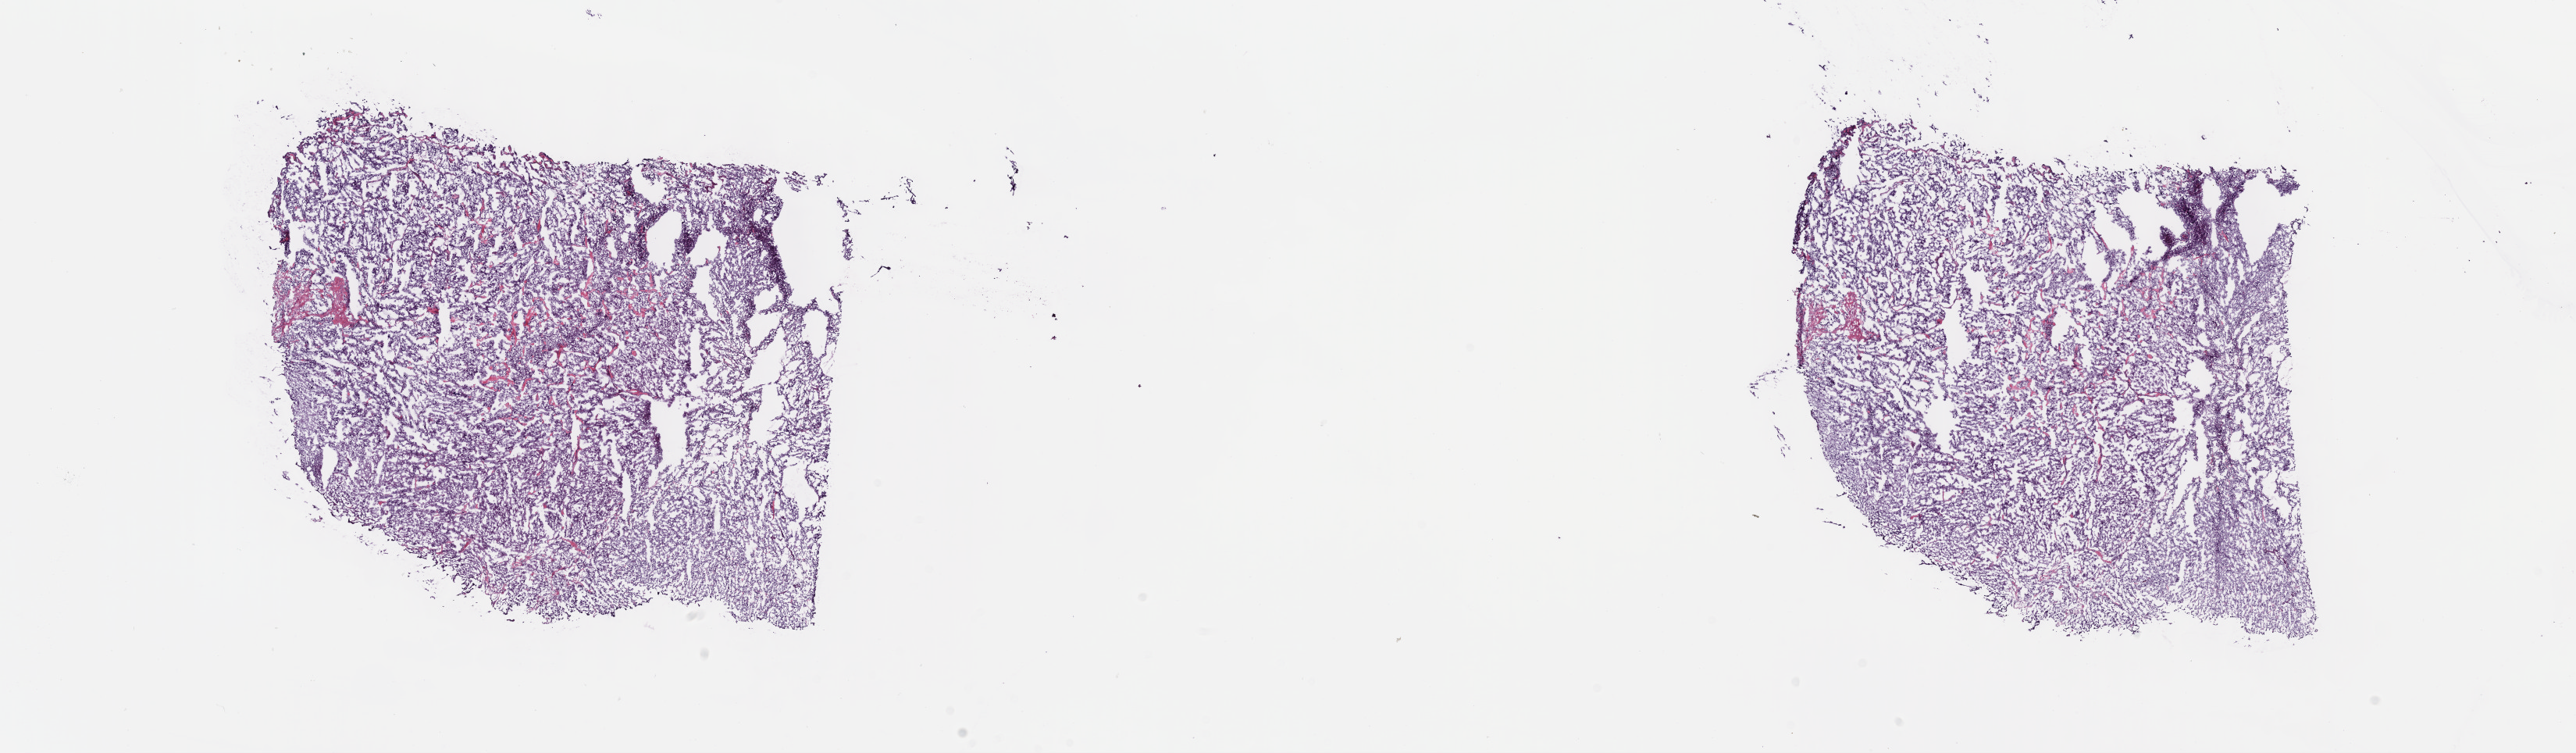
Whole-slide histology image, H&E-stained, shown as a low-resolution overview of the whole scanned area (about 26.7 x 7.8 mm), frozen section from the top of the tissue portion, primary tumour sample from the retroperitoneum and peritoneum. Patient: male, age at initial diagnosis 44 years. Slide review estimates, as recorded: tumour cells 90%, tumour nuclei 95%, normal cells 0%, stromal cells 10%, necrosis 0%. Infiltration values recorded for this section: lymphocyte infiltration 0%, monocyte infiltration 0%, neutrophil infiltration 0%.
* histologic diagnosis: Extra-adrenal paraganglioma, NOS (retroperitoneum)